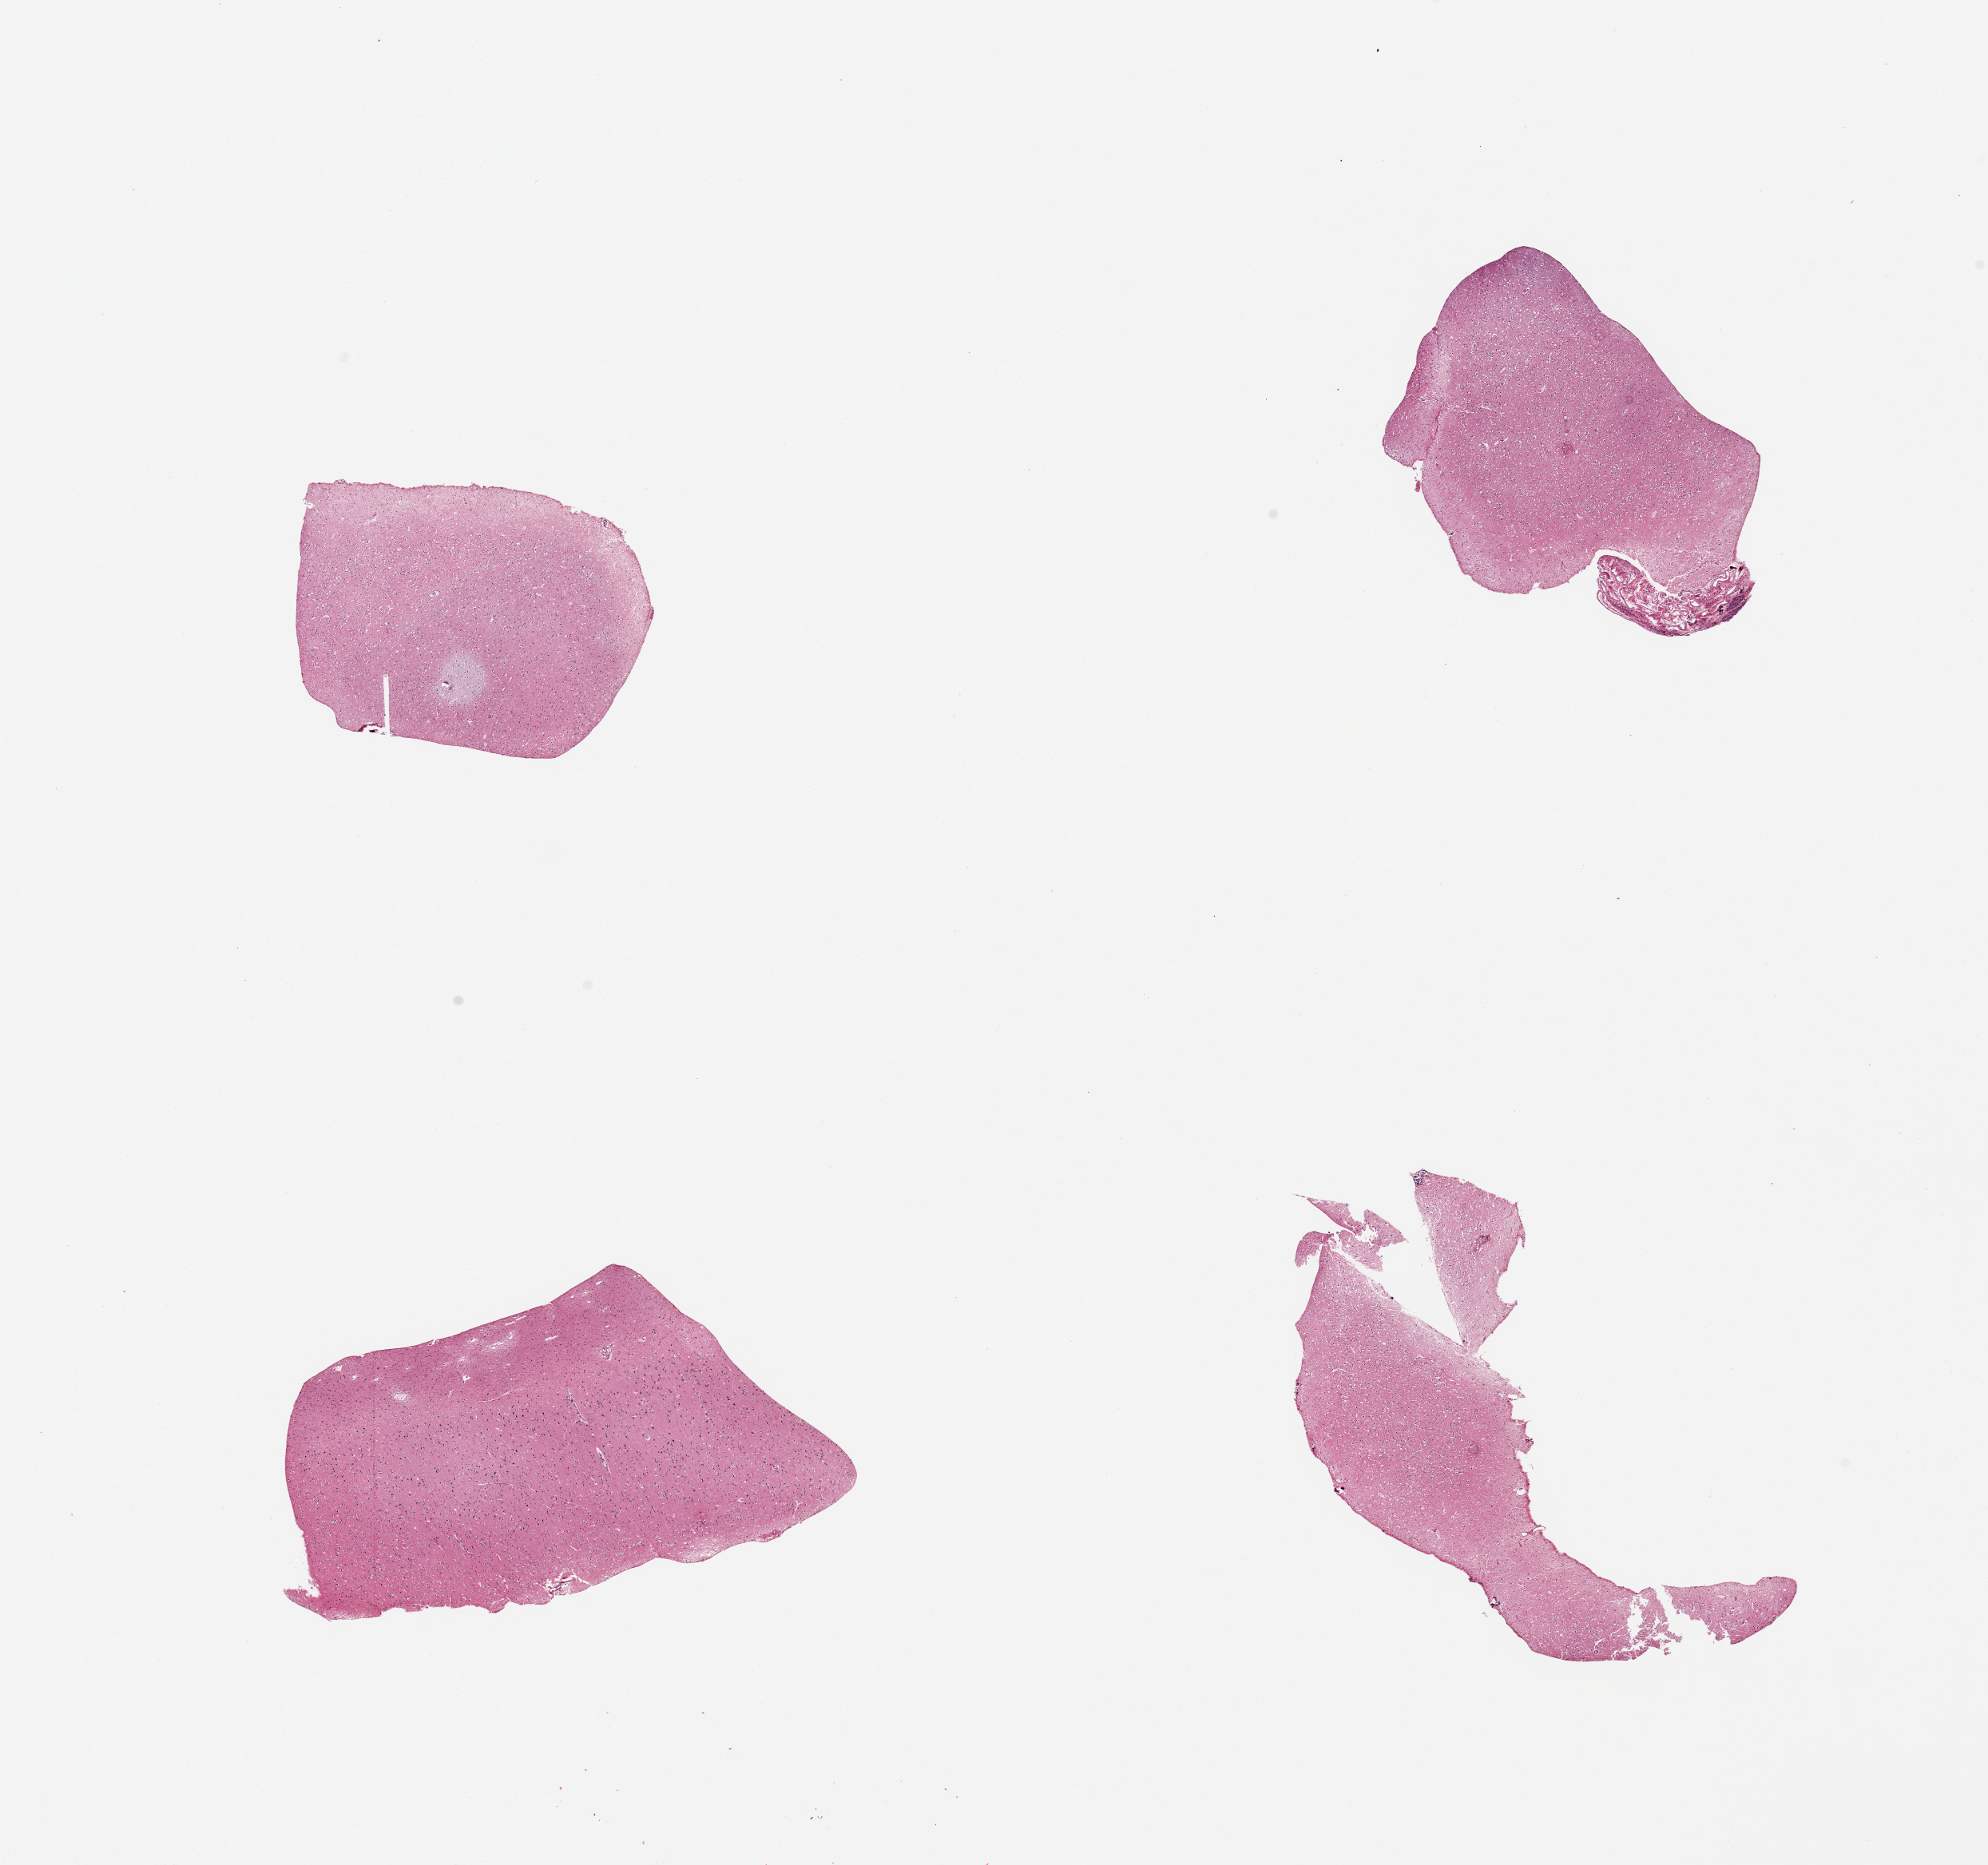
H&E whole-slide image — low-resolution overview of the scanned area, about 19.7 x 18.5 mm. PAXgene-fixed, paraffin-embedded tissue. Sampled site (target tissue): cerebral cortex. Tissue donor sample. Male donor.
* reviewer comment on this tissue sample: 4 pieces, no abnormalities